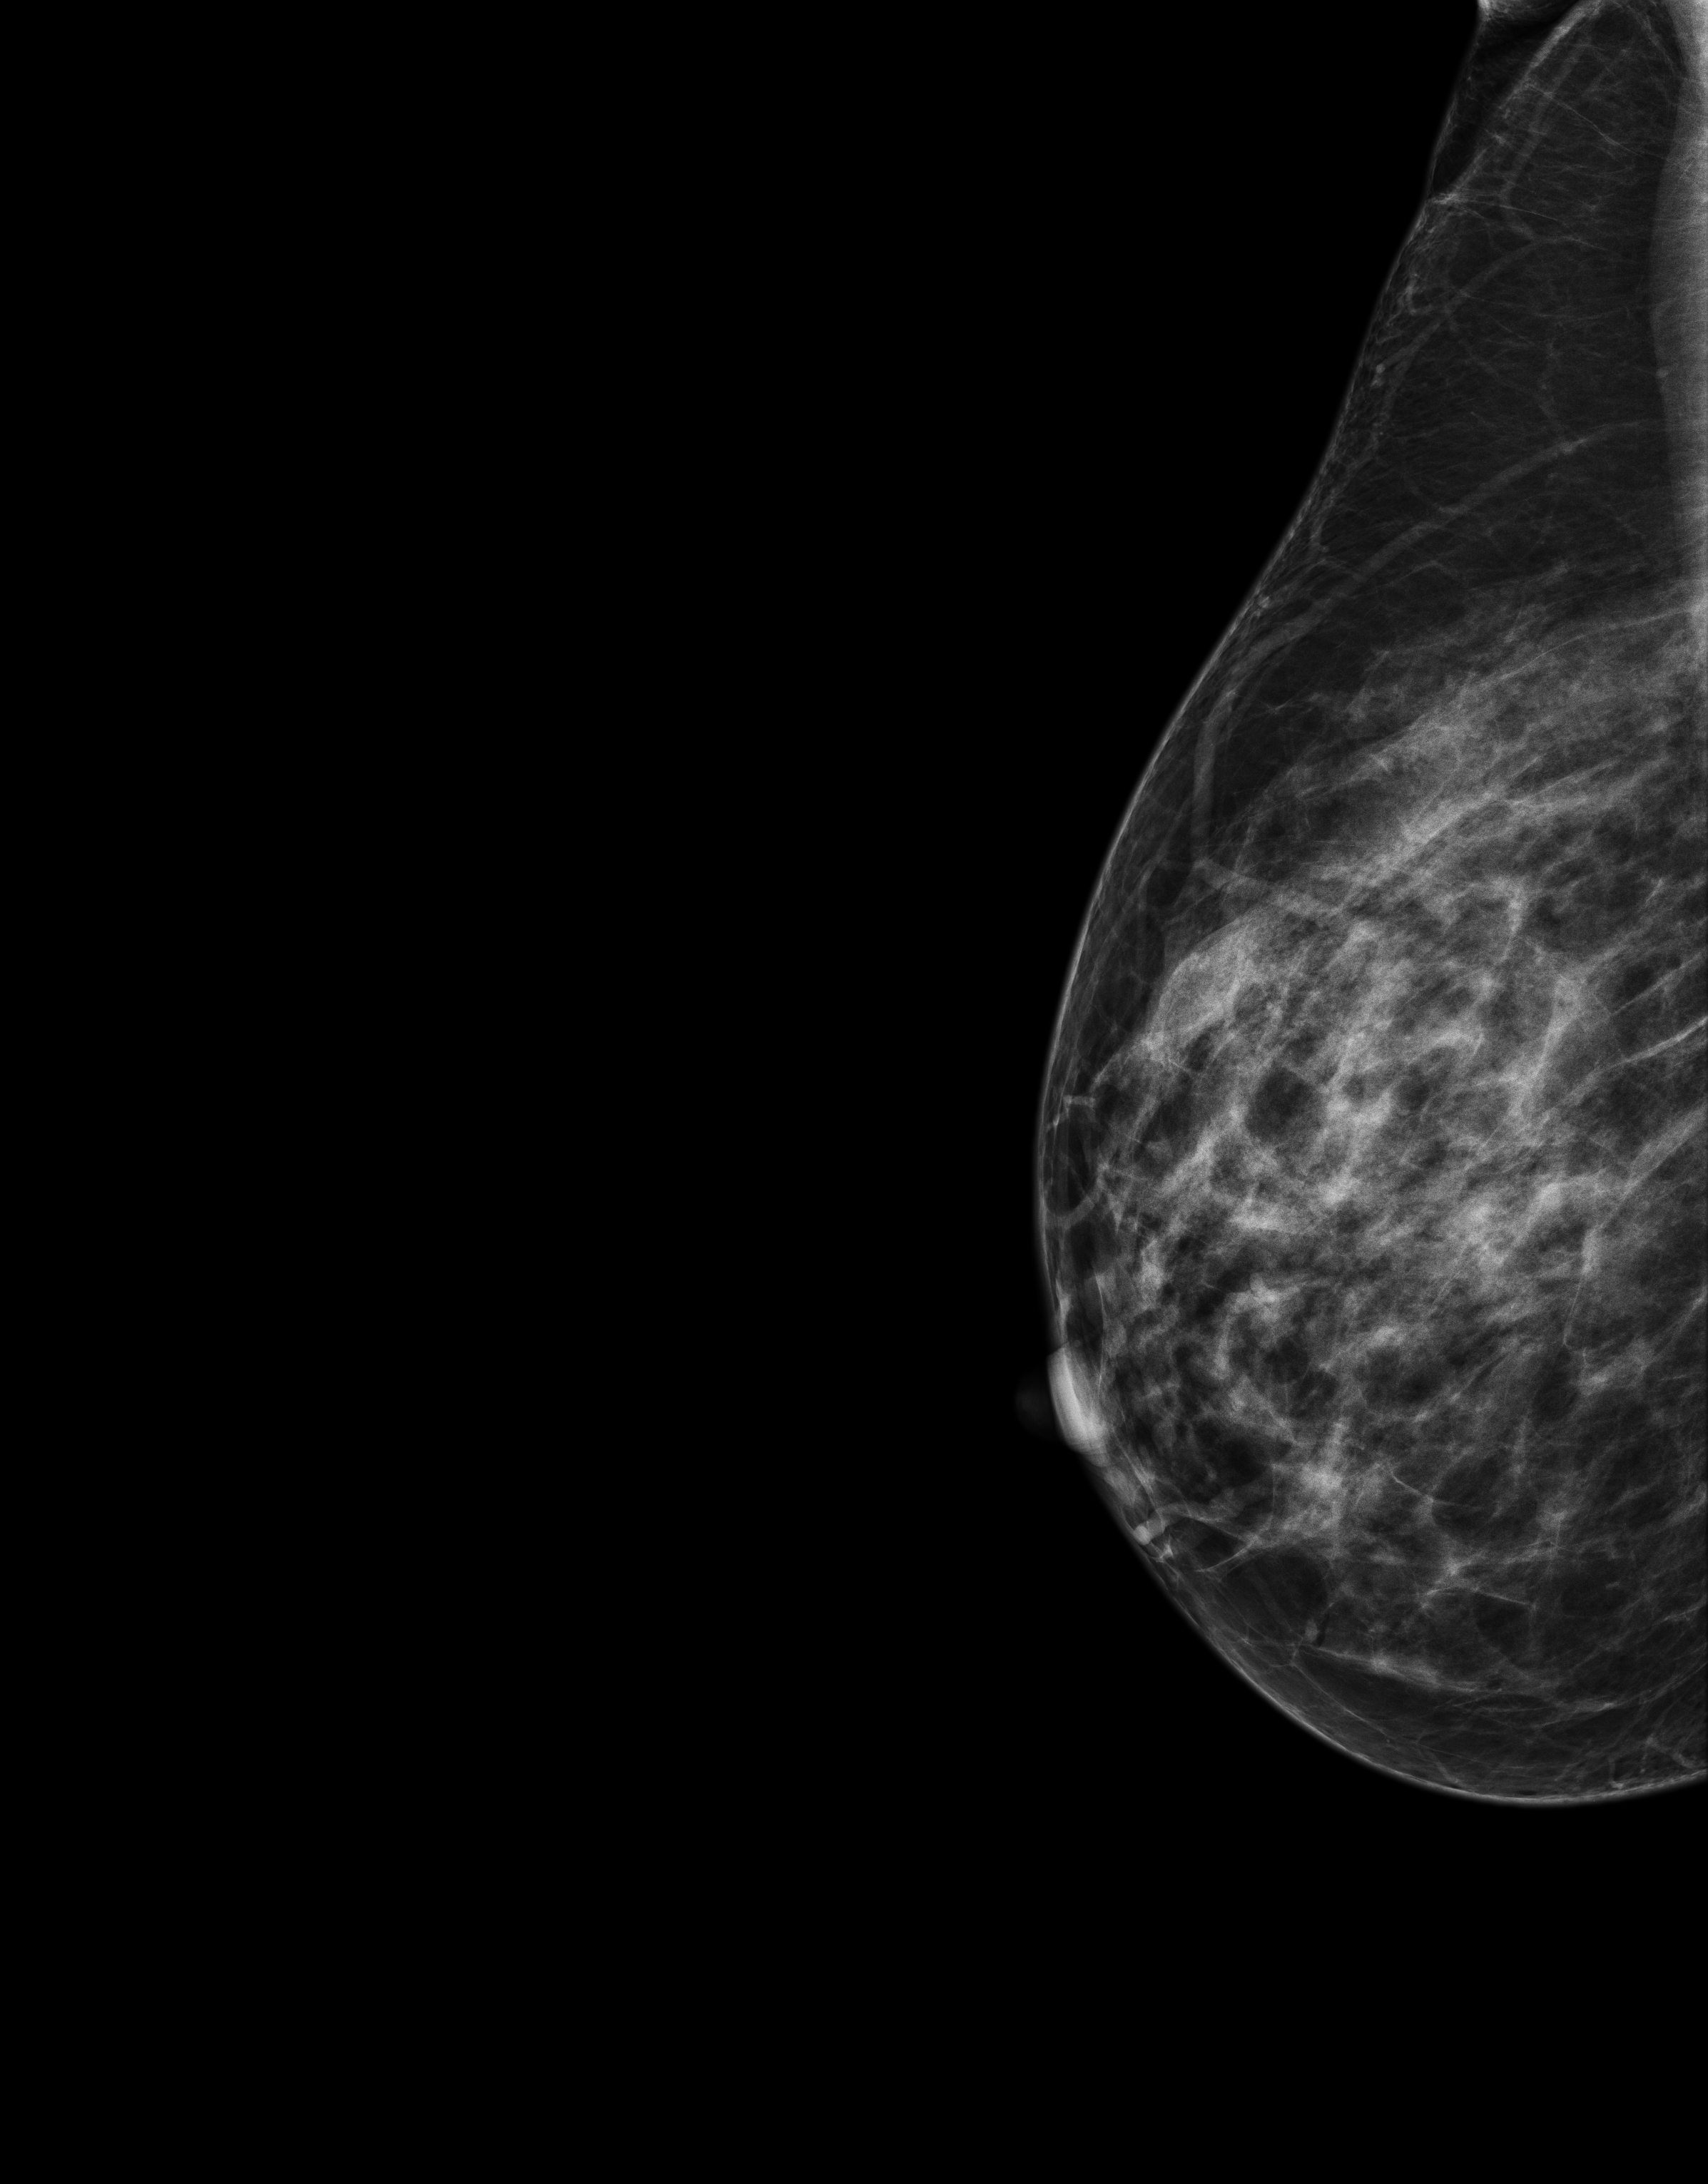
Full-field digital mammogram (FFDM), right breast, laterally exaggerated craniocaudal (XCCL) view, screening examination, compressed breast thickness 67 mm, system: Senographe Essential ADS_56.21.3. Patient: female, 49 years.
Breast density at the screening exam (both breasts): heterogeneously dense (BI-RADS density category c). Final BI-RADS category for the screening round (tomosynthesis exam, both breasts): category 1. Recall: no recall after this screen.